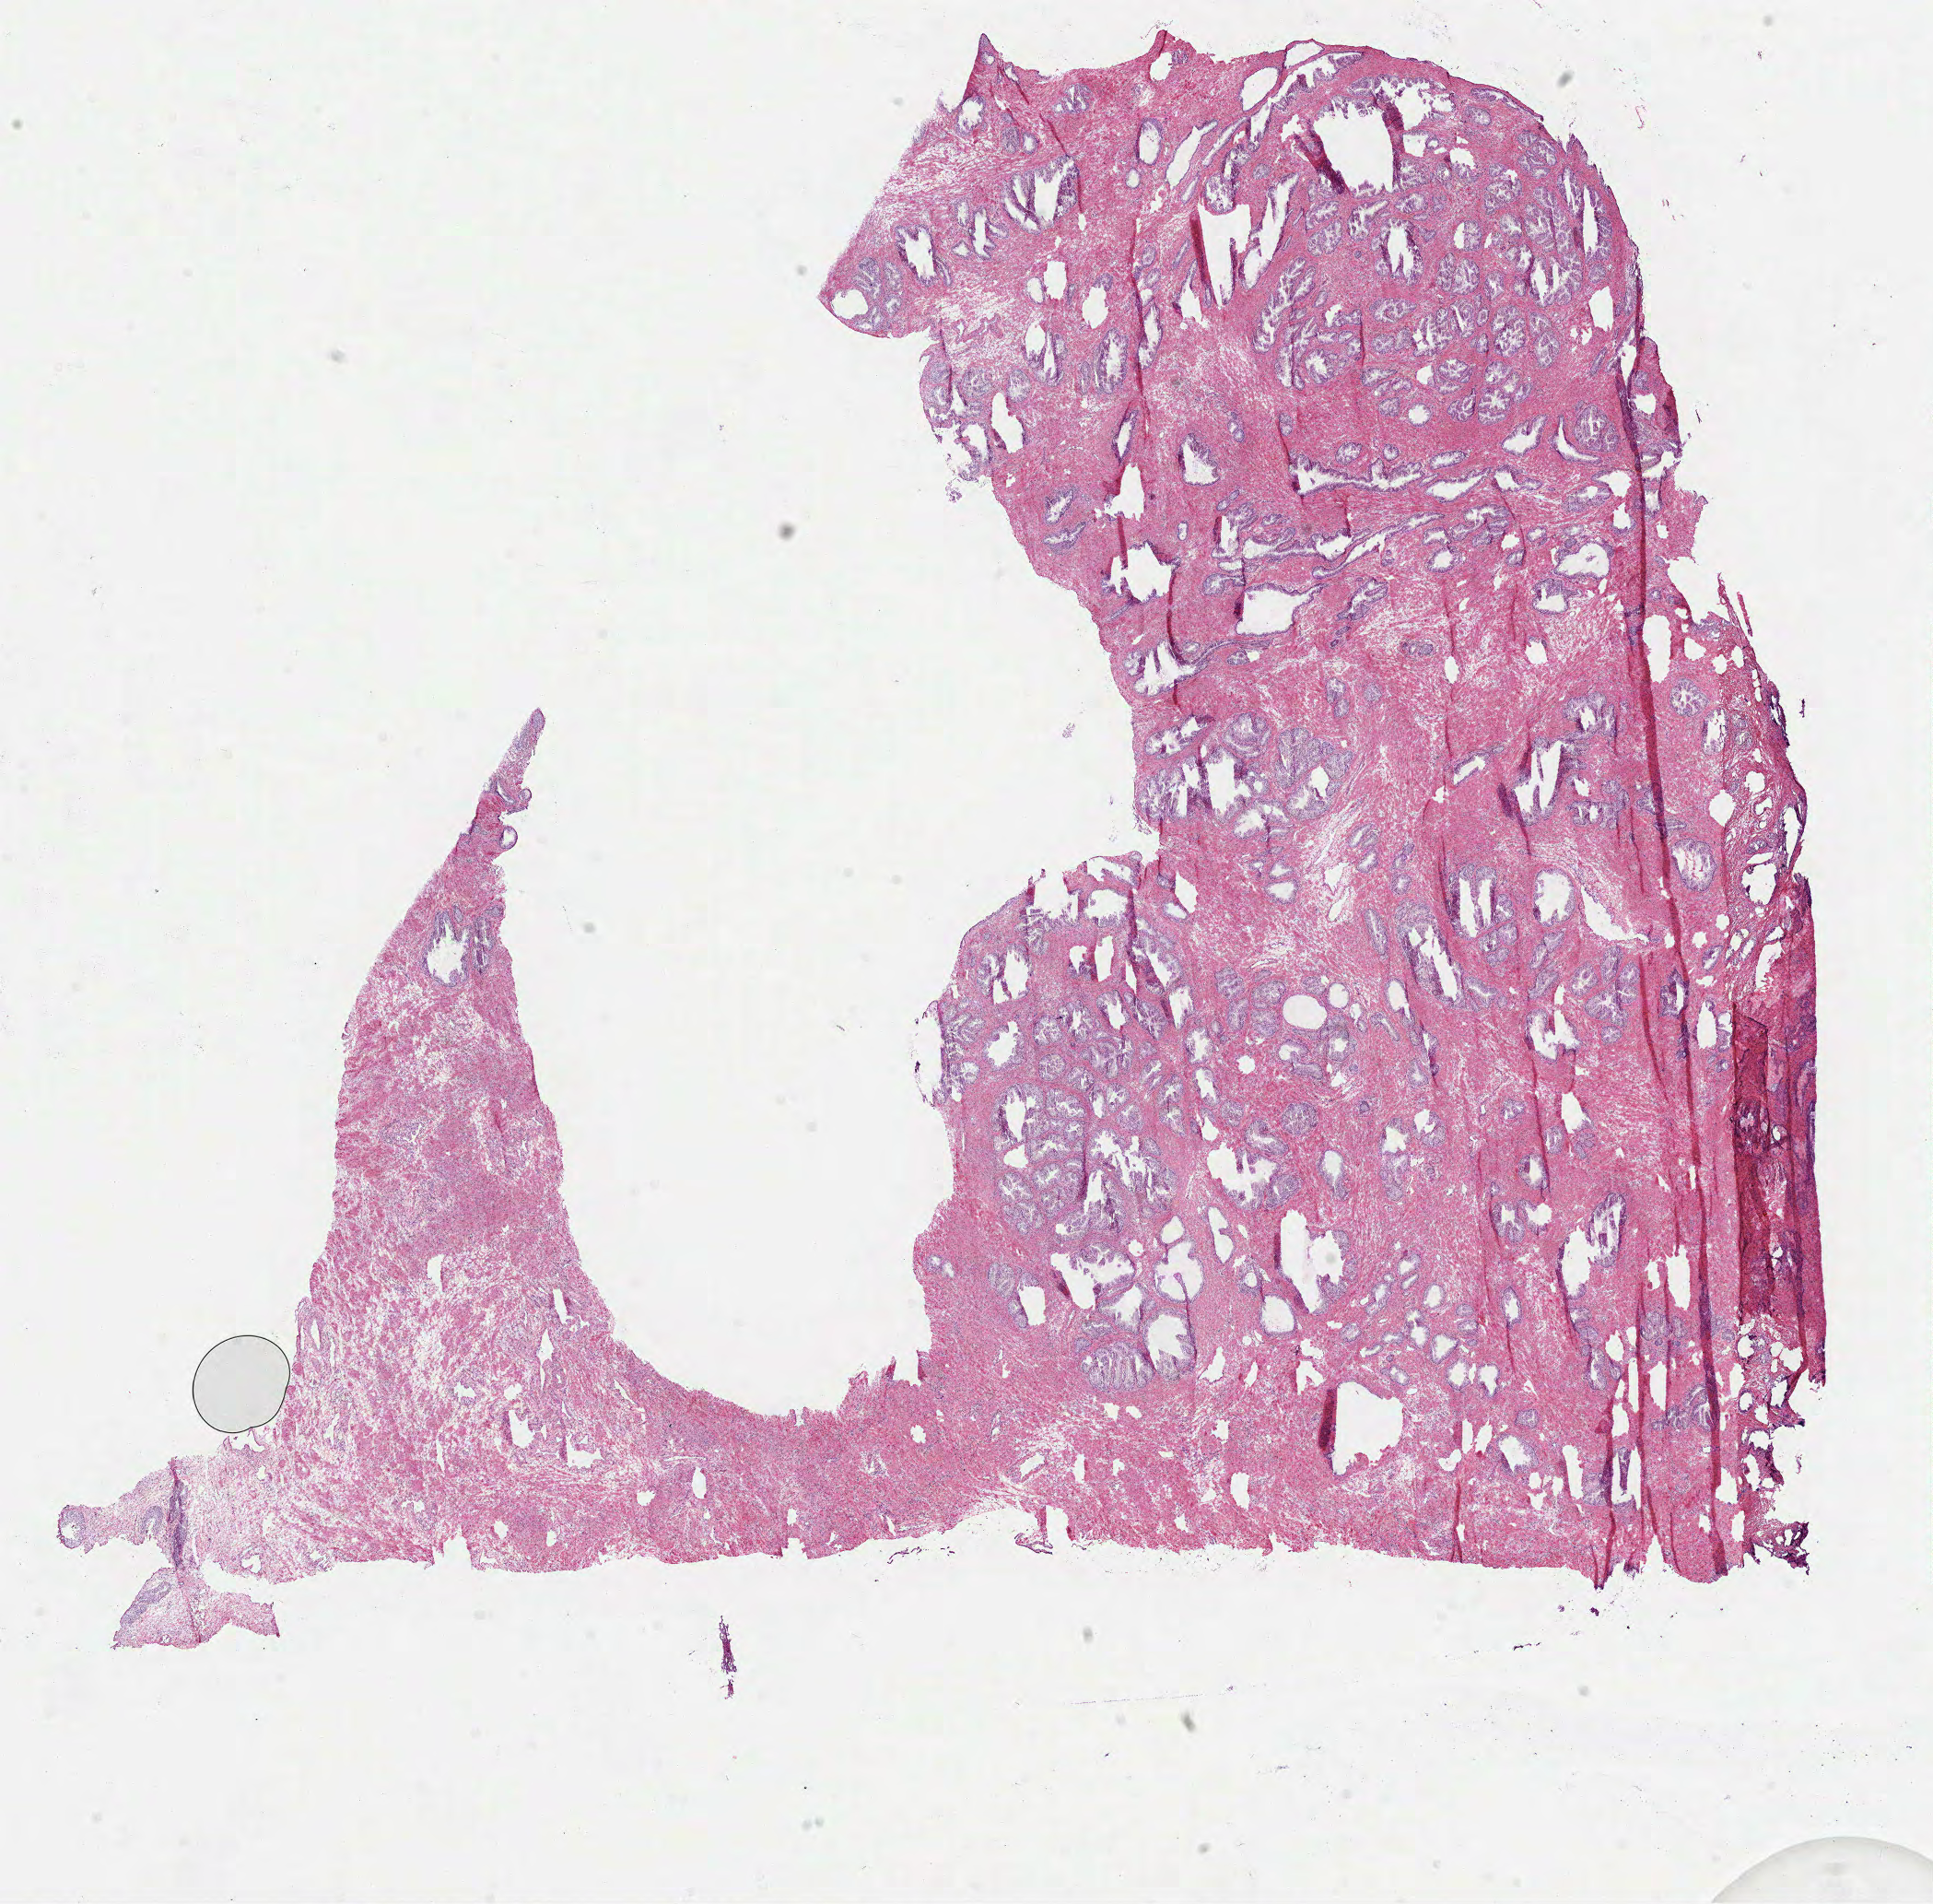
Whole-slide histology image, Hematoxylin and eosin (H&E) stained — low-resolution overview of the scanned area, about 16.9 x 16.7 mm (from a 40x scan). Frozen section. Sample: solid tissue normal (non-tumour tissue), prostate. Male, age 53 years at initial diagnosis.
This section: solid tissue normal (non-tumour) sample from the same patient. Patient diagnosis: Acinar cell carcinoma (prostate gland).